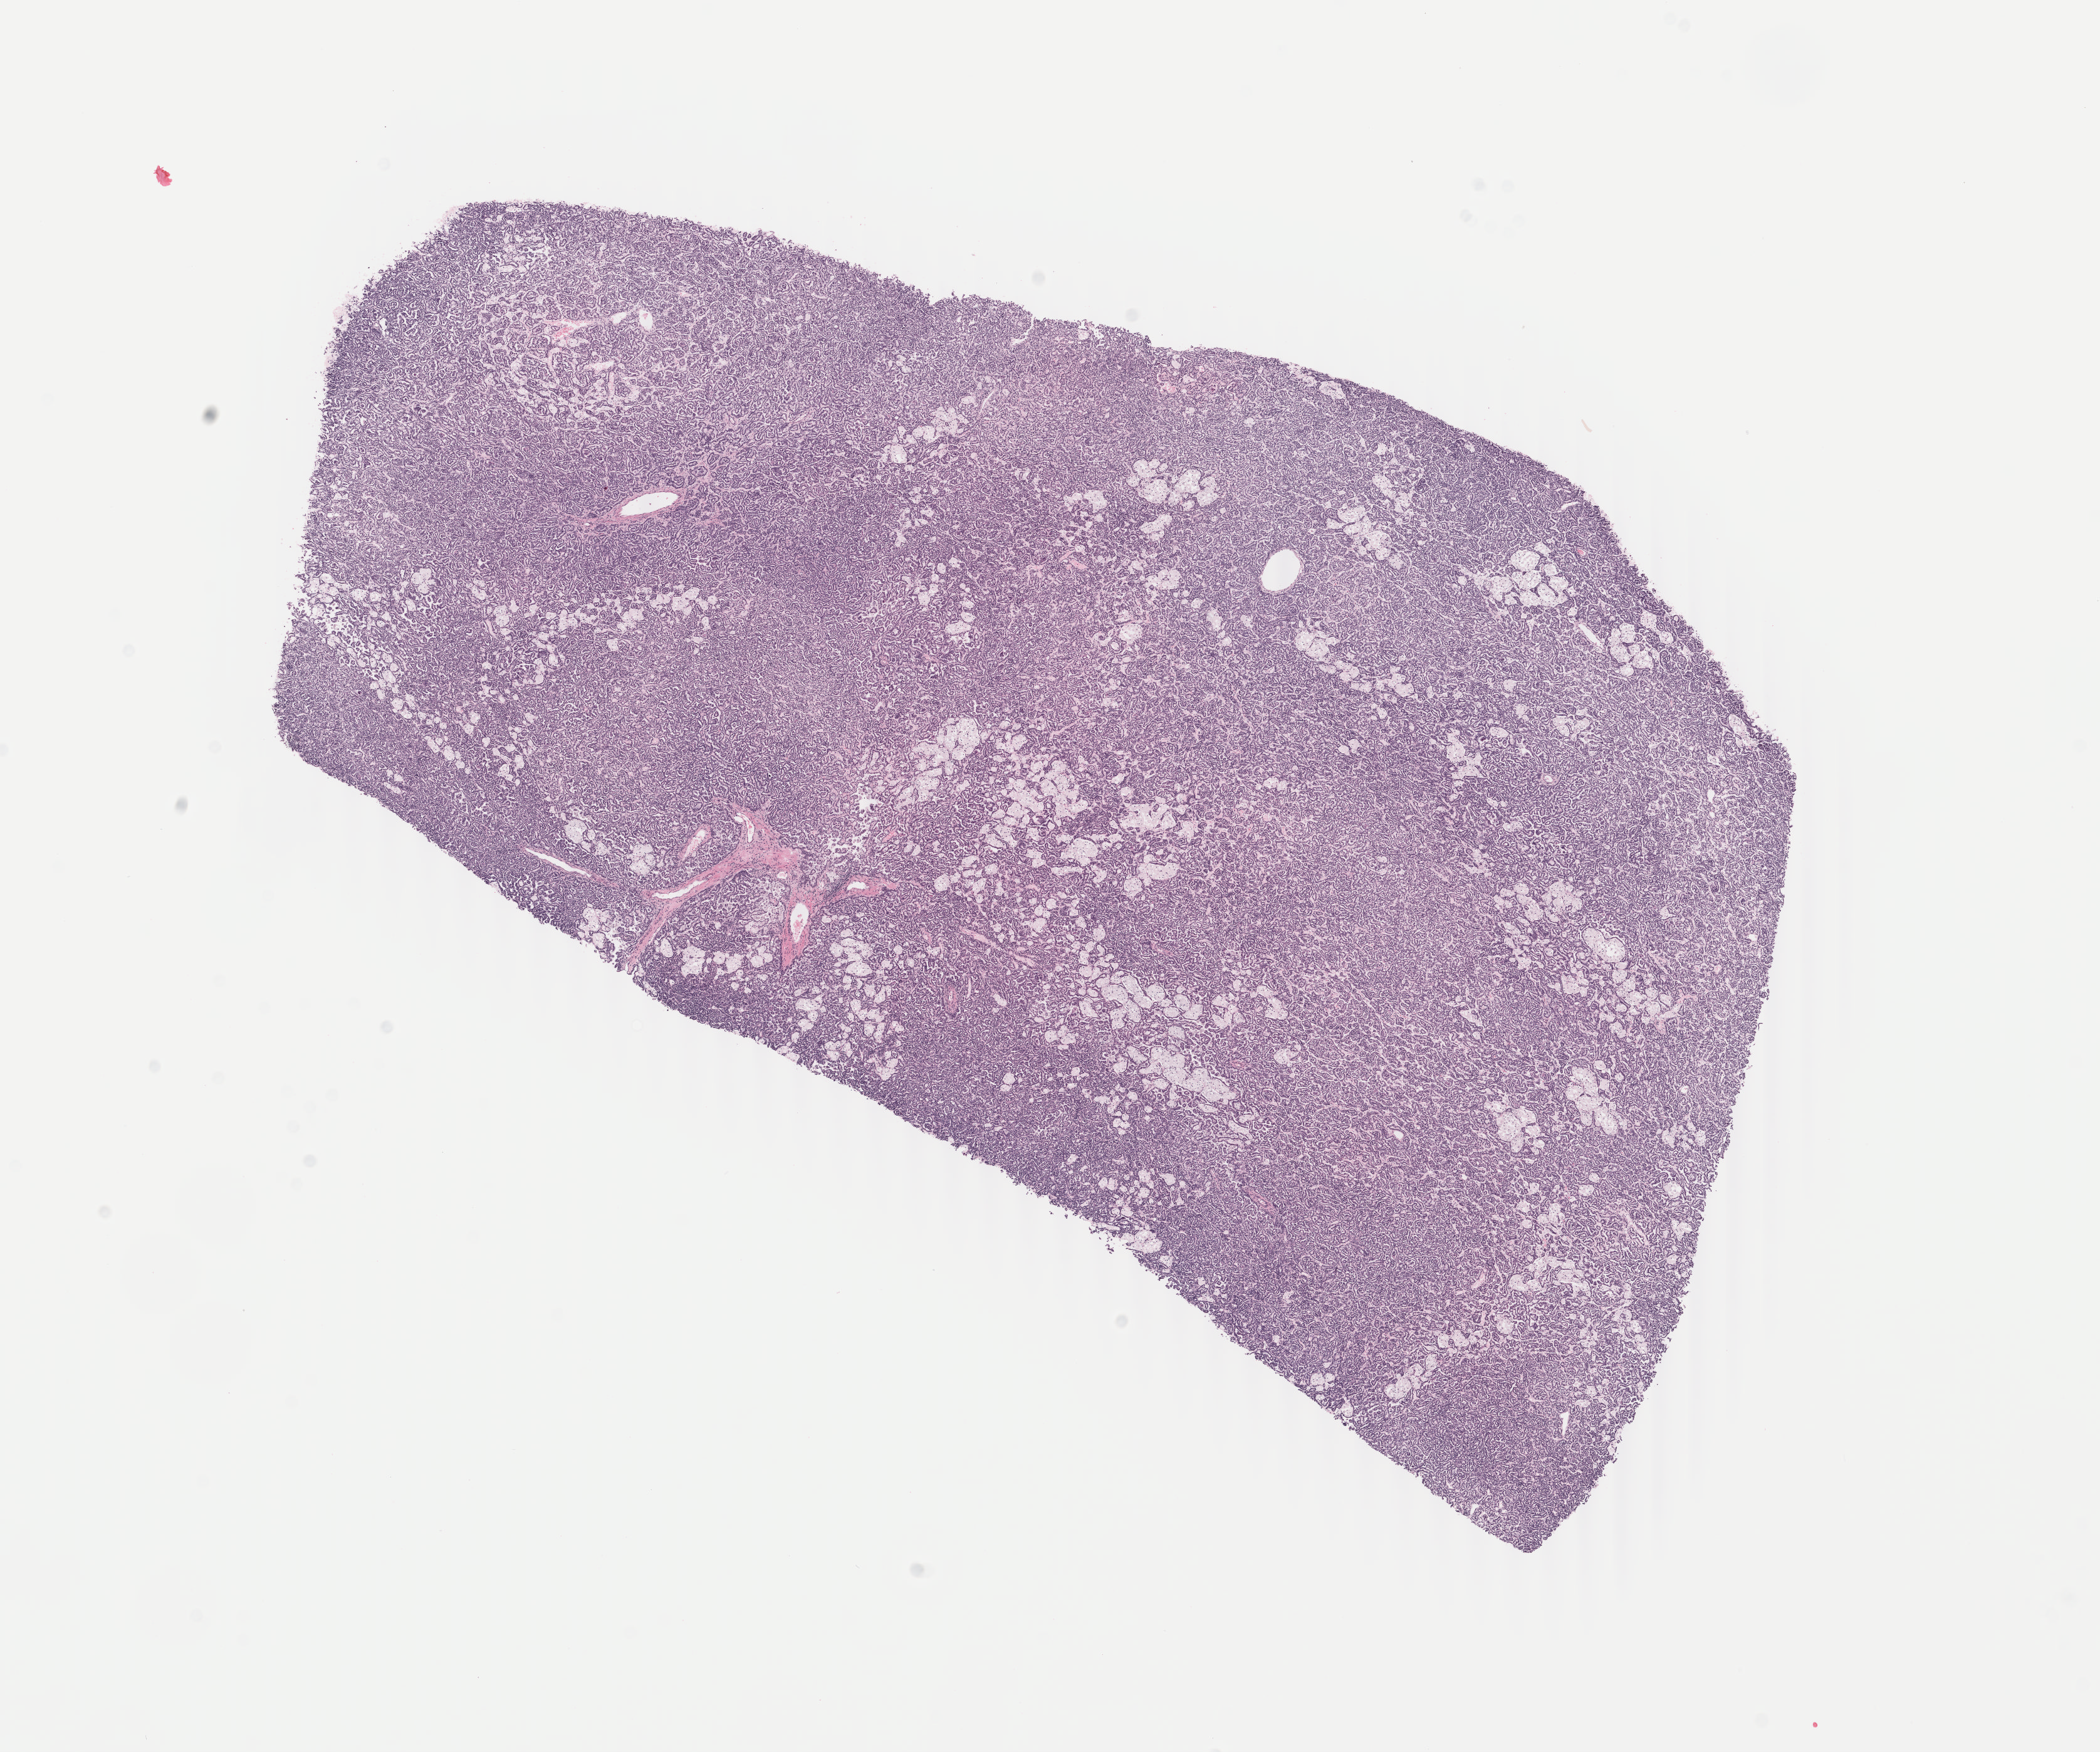
Whole-slide histology image, Hematoxylin and eosin (H&E) stained, shown as a low-resolution overview of the whole scanned area (about 13.3 x 11.1 mm), formalin-fixed paraffin-embedded (FFPE) diagnostic section, primary tumour sample from the kidney. Patient: male, age at initial diagnosis 57 years.
Laterality: left. Histologic diagnosis: Papillary adenocarcinoma, NOS.